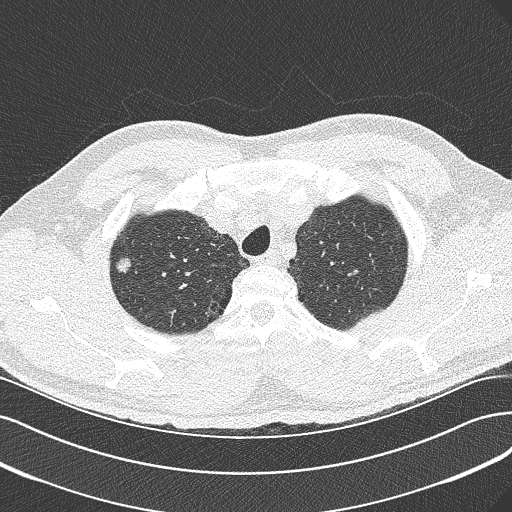
Chest CT (low-dose screening protocol), one axial image, baseline screening round, lung window (W 1500 / L -600 HU), lung (sharp) reconstruction kernel (B50f), slice 47 of 342 in the series. Male, age 56 years at enrolment. Current smoker at enrolment.
• Expert-annotated lung lesion, bounding box <104,248,142,284> (left, top, right, bottom; pixels).
• Screening reader's record for this exam (one nodule recorded; not confirmed to be the boxed lesion): non-calcified nodule or mass ≥4 mm, right upper lobe, 10 × 7 mm, spiculated (stellate) margins, soft tissue attenuation.
• Official screen result: positive, change unspecified: nodule(s) >= 4 mm or enlarging nodule(s), mass(es), or other non-specific abnormalities suspicious for lung cancer.
• Later outcome: lung cancer diagnosed 517 days after this screen (after the second annual screen) — bronchiolo-alveolar carcinoma, non-mucinous, right upper lobe, moderately differentiated (G2), stage IIIB (AJCC 6th edition), 10 mm at pathology.